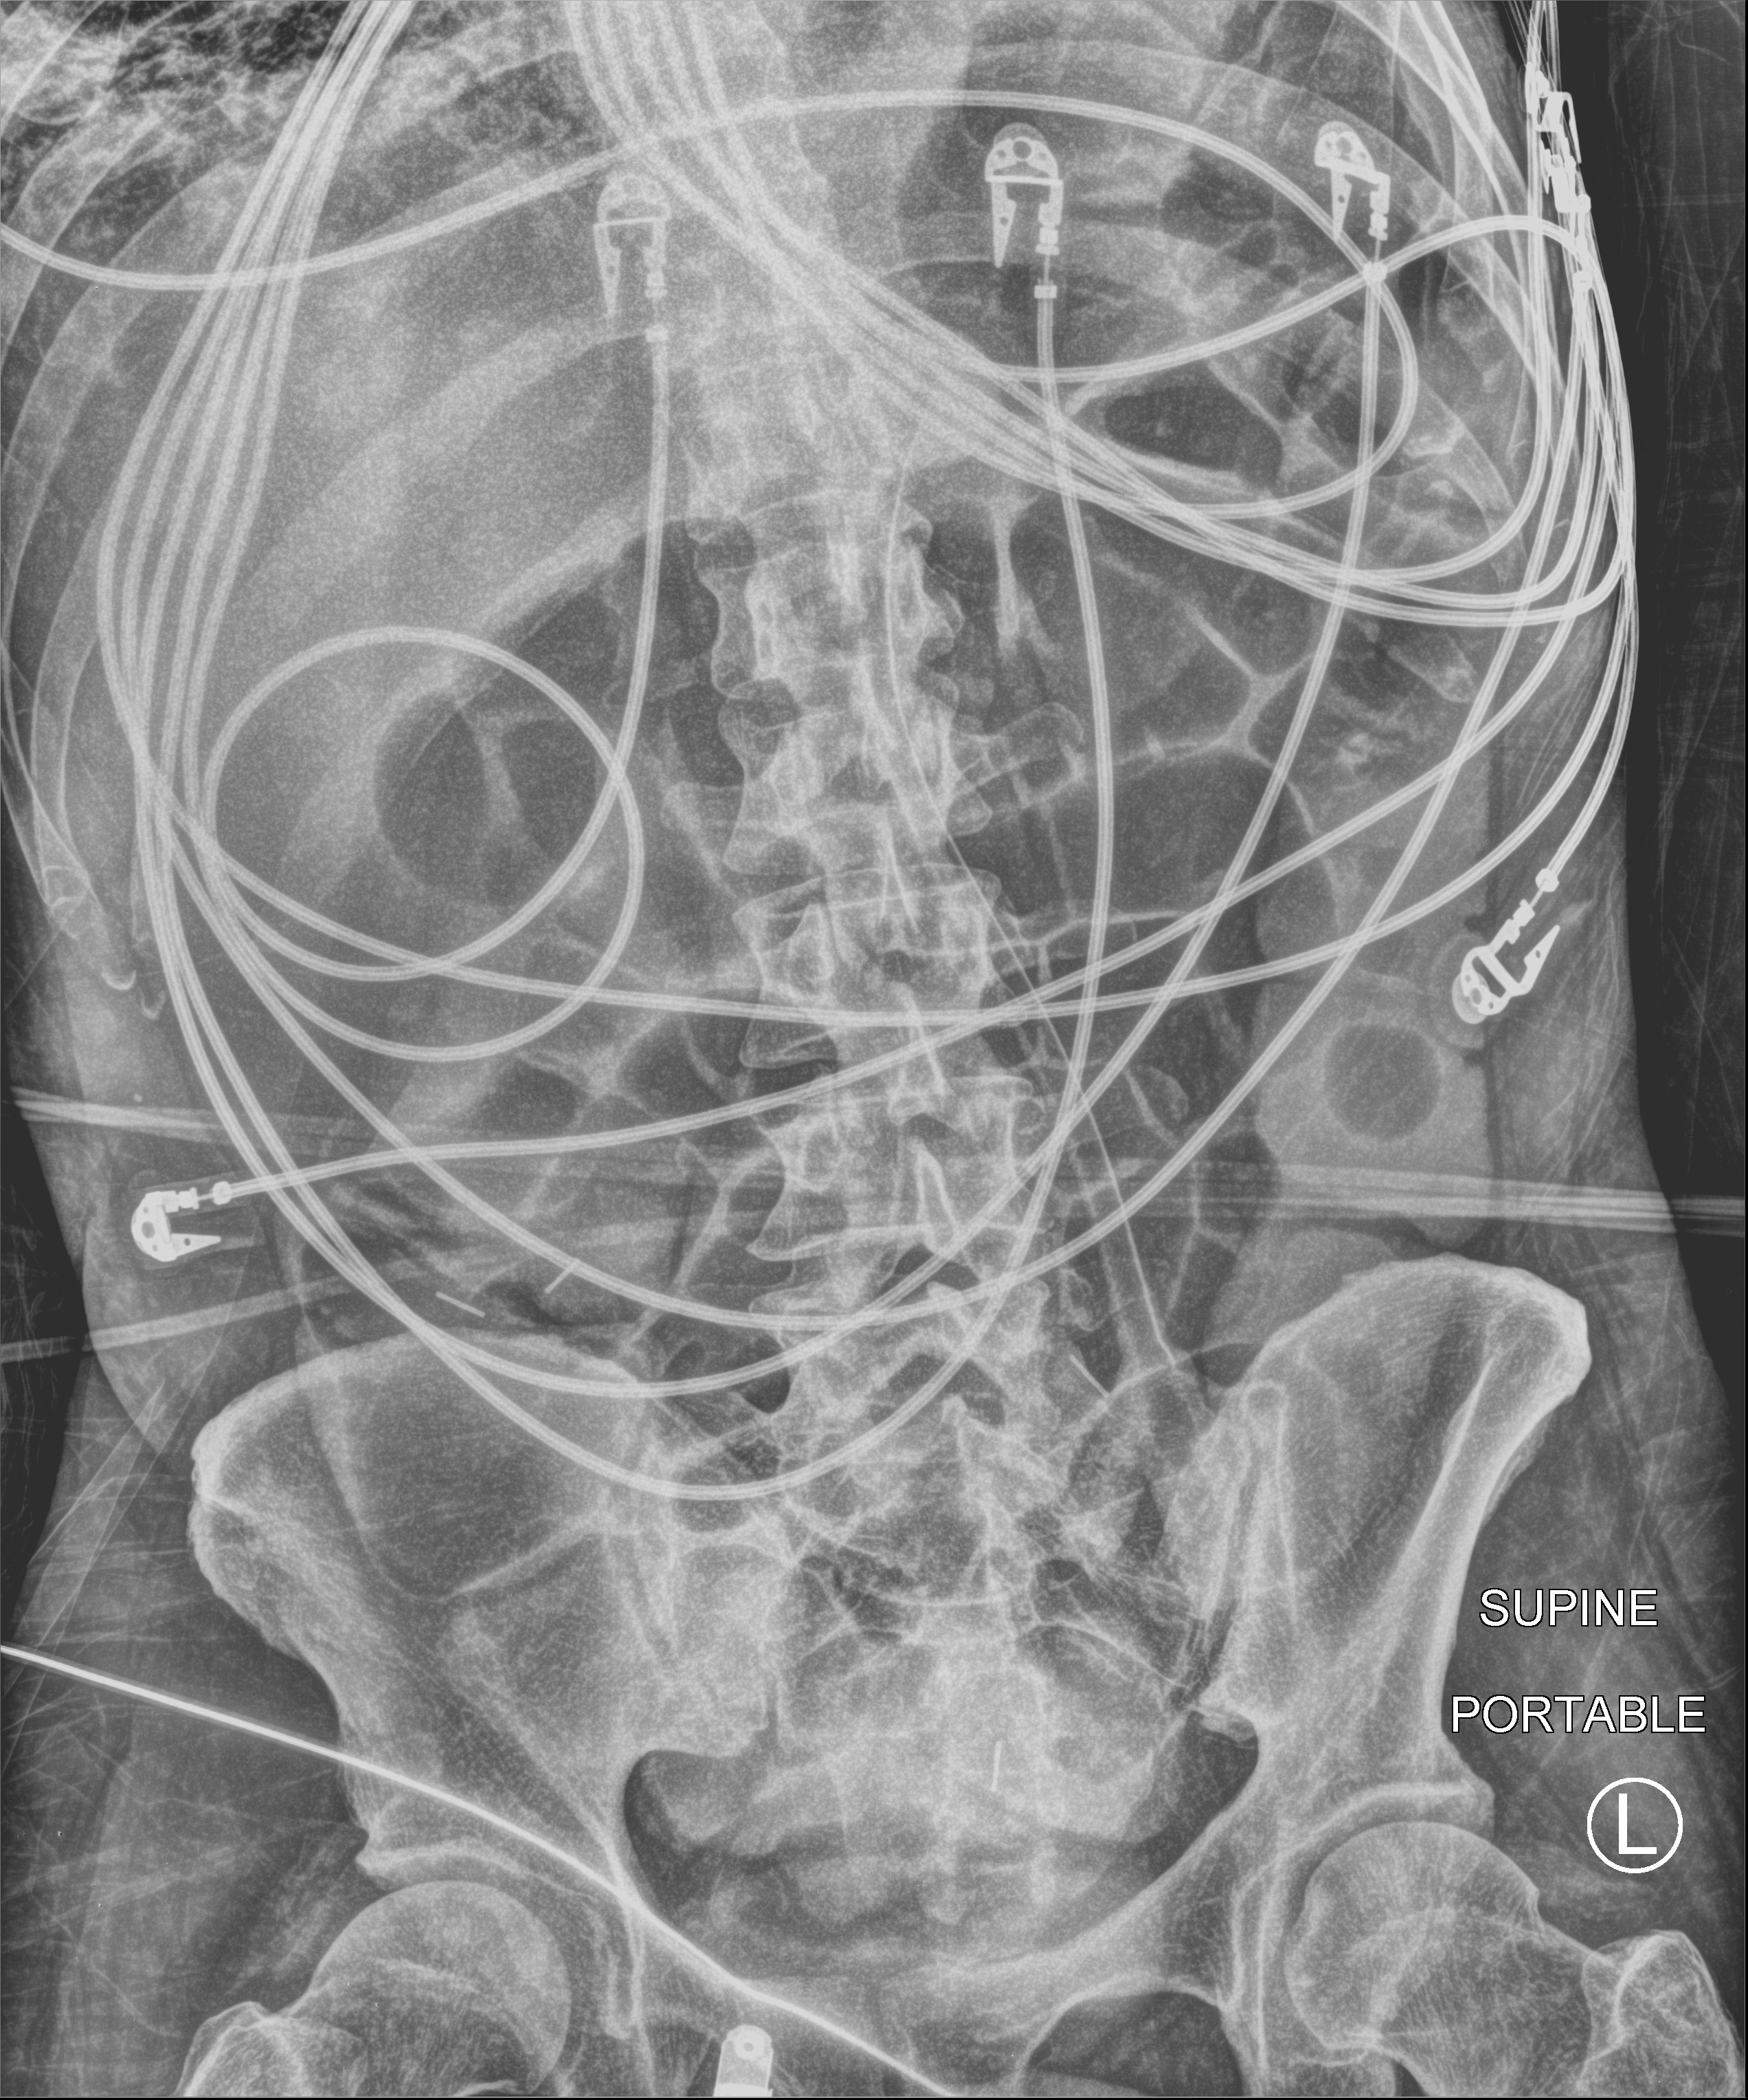
Bedside abdomen radiograph (computed radiography), anteroposterior (AP) projection. Male patient hospitalised with COVID-19, age 18–59 years.
From the hospital-stay record, not from the radiograph (when in the stay this image was taken is not recorded): chronic kidney disease (admission record): no; admitted to intensive care during this hospital stay: yes; COPD (admission record): no.